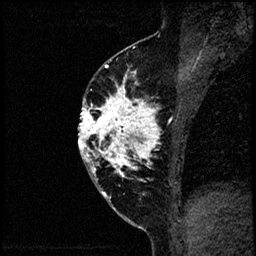
Breast MRI (dynamic contrast-enhanced), one sagittal slice; dynamic contrast-enhanced study with each time point stored as its own series, time point 2 of 4 at this slice position (early post-contrast, ordered by acquisition time); 1.5 T; TE 4.2 ms, TR 17.6 ms; 2 mm slice thickness; 256 × 256 image matrix, field of view 200 × 200 mm. Patient: female, 40 years. From the clinical record (not read from this slice): setting: breast cancer imaged before/during neoadjuvant chemotherapy; receptor status: HER2-positive.
Structures marked on this image (semi-automatically segmented with operator editing):
- analysis volume of interest (the breast-tissue region the enhancement analysis was run in; not a lesion): box from (x=79, y=56) to (x=197, y=205) px
- tumour enhancement mask (voxels above the 100 % enhancement threshold inside the analysis volume of interest): (x=80, y=59)–(x=197, y=195)